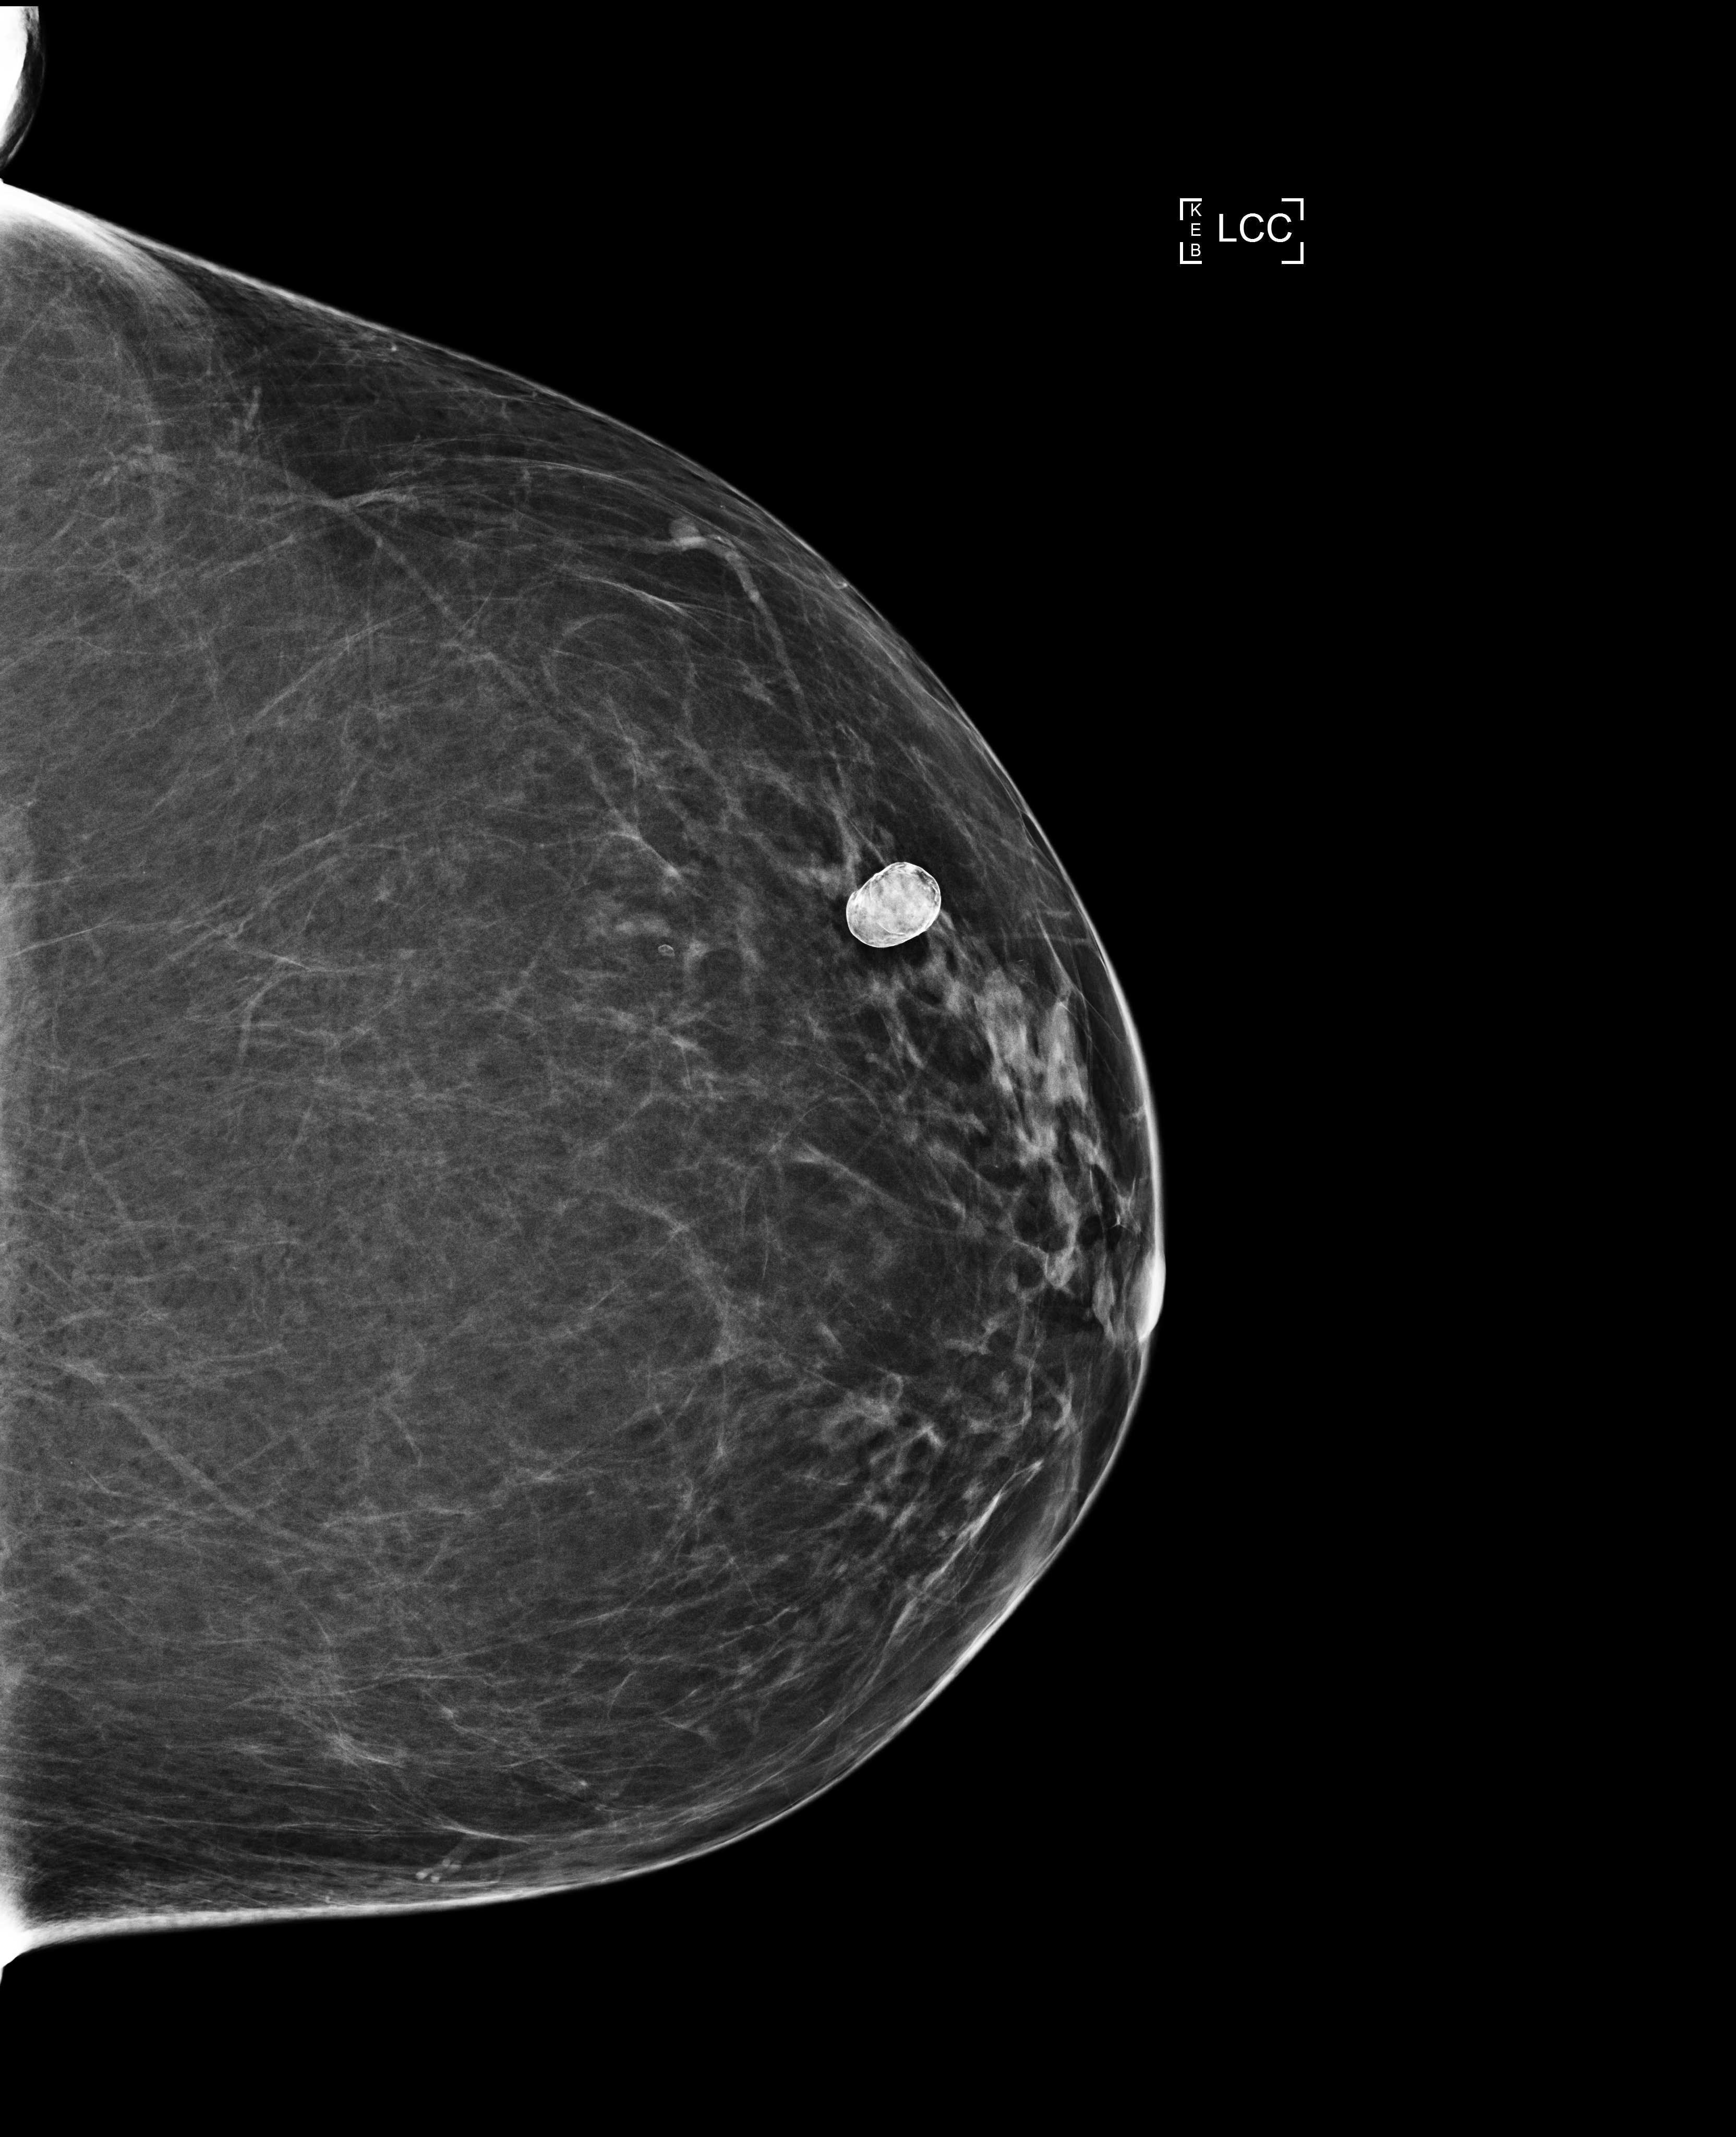
Screening examination; system: Selenia Dimensions. Patient: female, 67 years.
Image type: full-field digital mammogram. Breast: left. Projection: CC view.